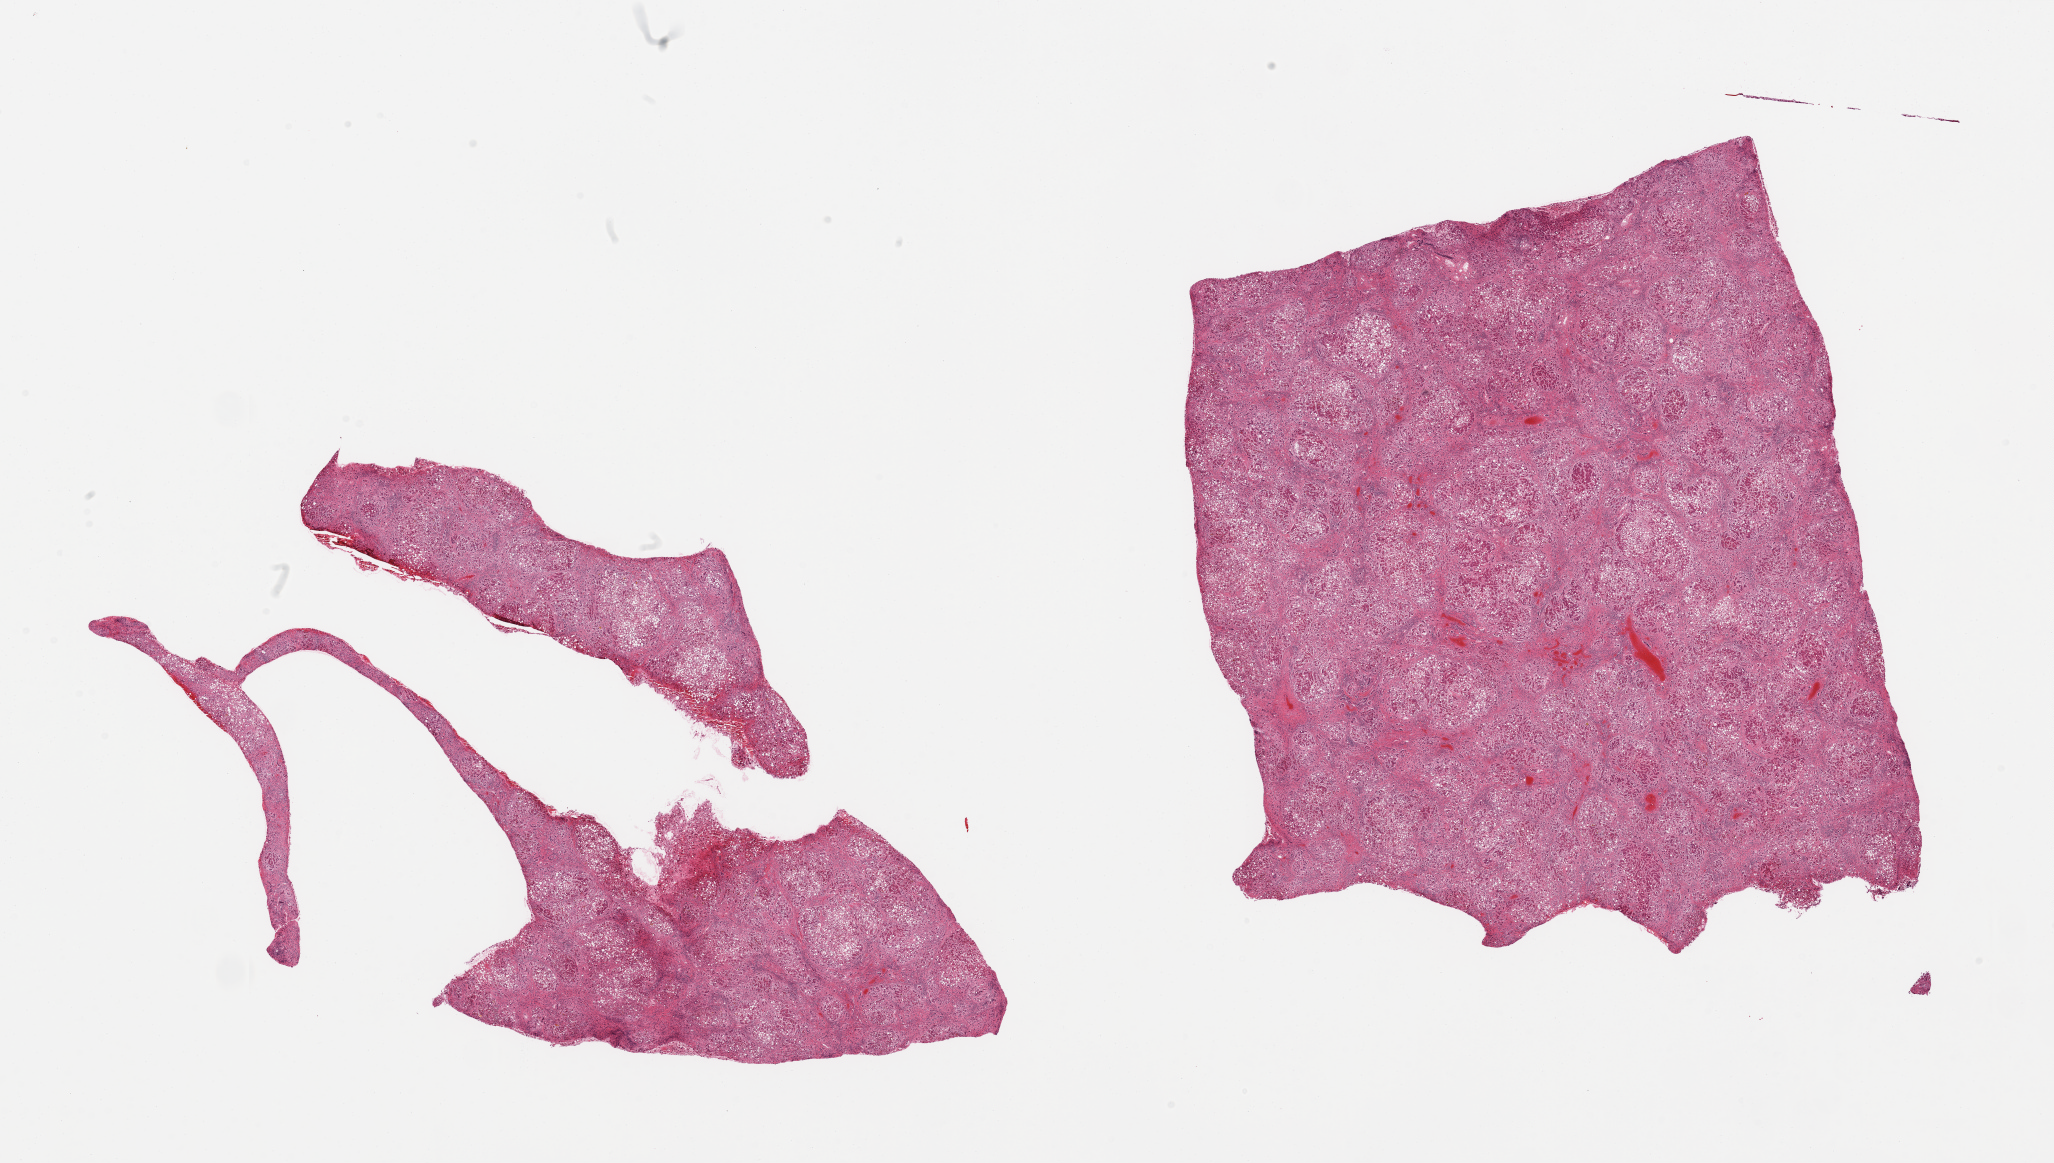
Digitized haematoxylin and eosin-stained section, brightfield — whole scanned area (about 32.5 x 18.4 mm, acquisition: 20x scan) shown as a low-resolution overview; PAXgene-fixed paraffin-embedded (PFPE) section; target tissue: liver; donor tissue sample. Donor sex: male.
- pathologist's review note for this sample: 2 pieces diffuse established cirrhosis, and macrovesicular steatosis